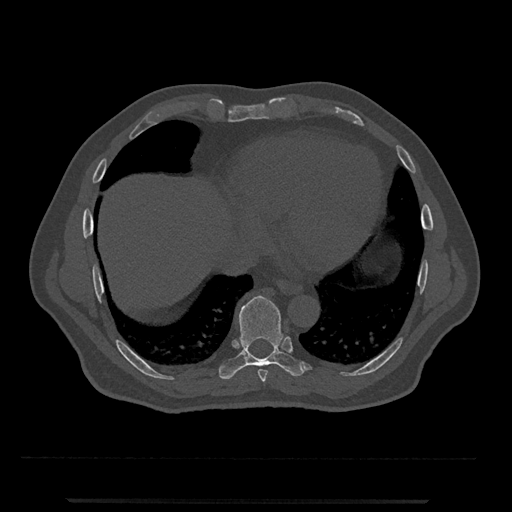
CT including the spine, one axial slice; position 585 of 797 along the scan axis; 120 kVp; bone window (W 1800 / L 400 HU); 0.5 mm slice thickness; 512 × 512 image matrix, field of view 419 × 419 mm. Patient: male, 63 years. Case-level facts recorded for this patient, not image findings: primary cancer: prostate.
Outlined on this slice (semi-automatically segmented with operator editing):
- T8 vertebra: bounding box (x1, y1, x2, y2) in pixels: (257, 369, 268, 382)
- T9 vertebra: (219, 296, 307, 380)